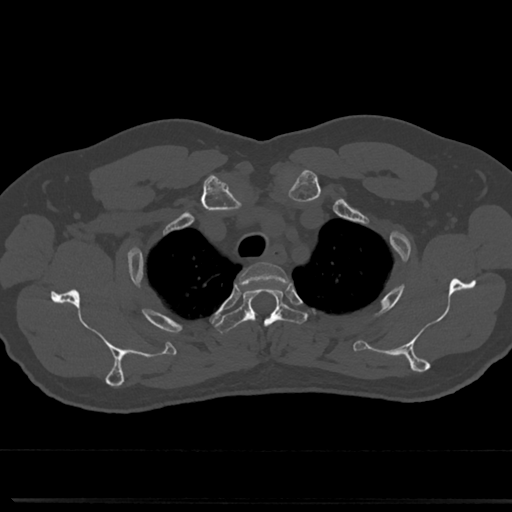
CT including the spine, one axial slice. Slice 604 of 817 in the series (ordered by position). Reconstruction kernel Br40s/3. 120 kVp. Bone window (W 1800 / L 400 HU). 0.5 mm slice thickness. 512 × 512 image matrix, field of view 355 × 355 mm. Male patient, age 61 years. From the clinical record (not read from this slice): primary cancer: prostate.
Annotated regions visible in this slice (semi-automatic segmentation, software-assisted and operator-edited):
- T2 vertebra: bounding box (x1, y1, x2, y2) in pixels: (243, 262, 287, 281)
- T3 vertebra: (216, 284, 301, 336)